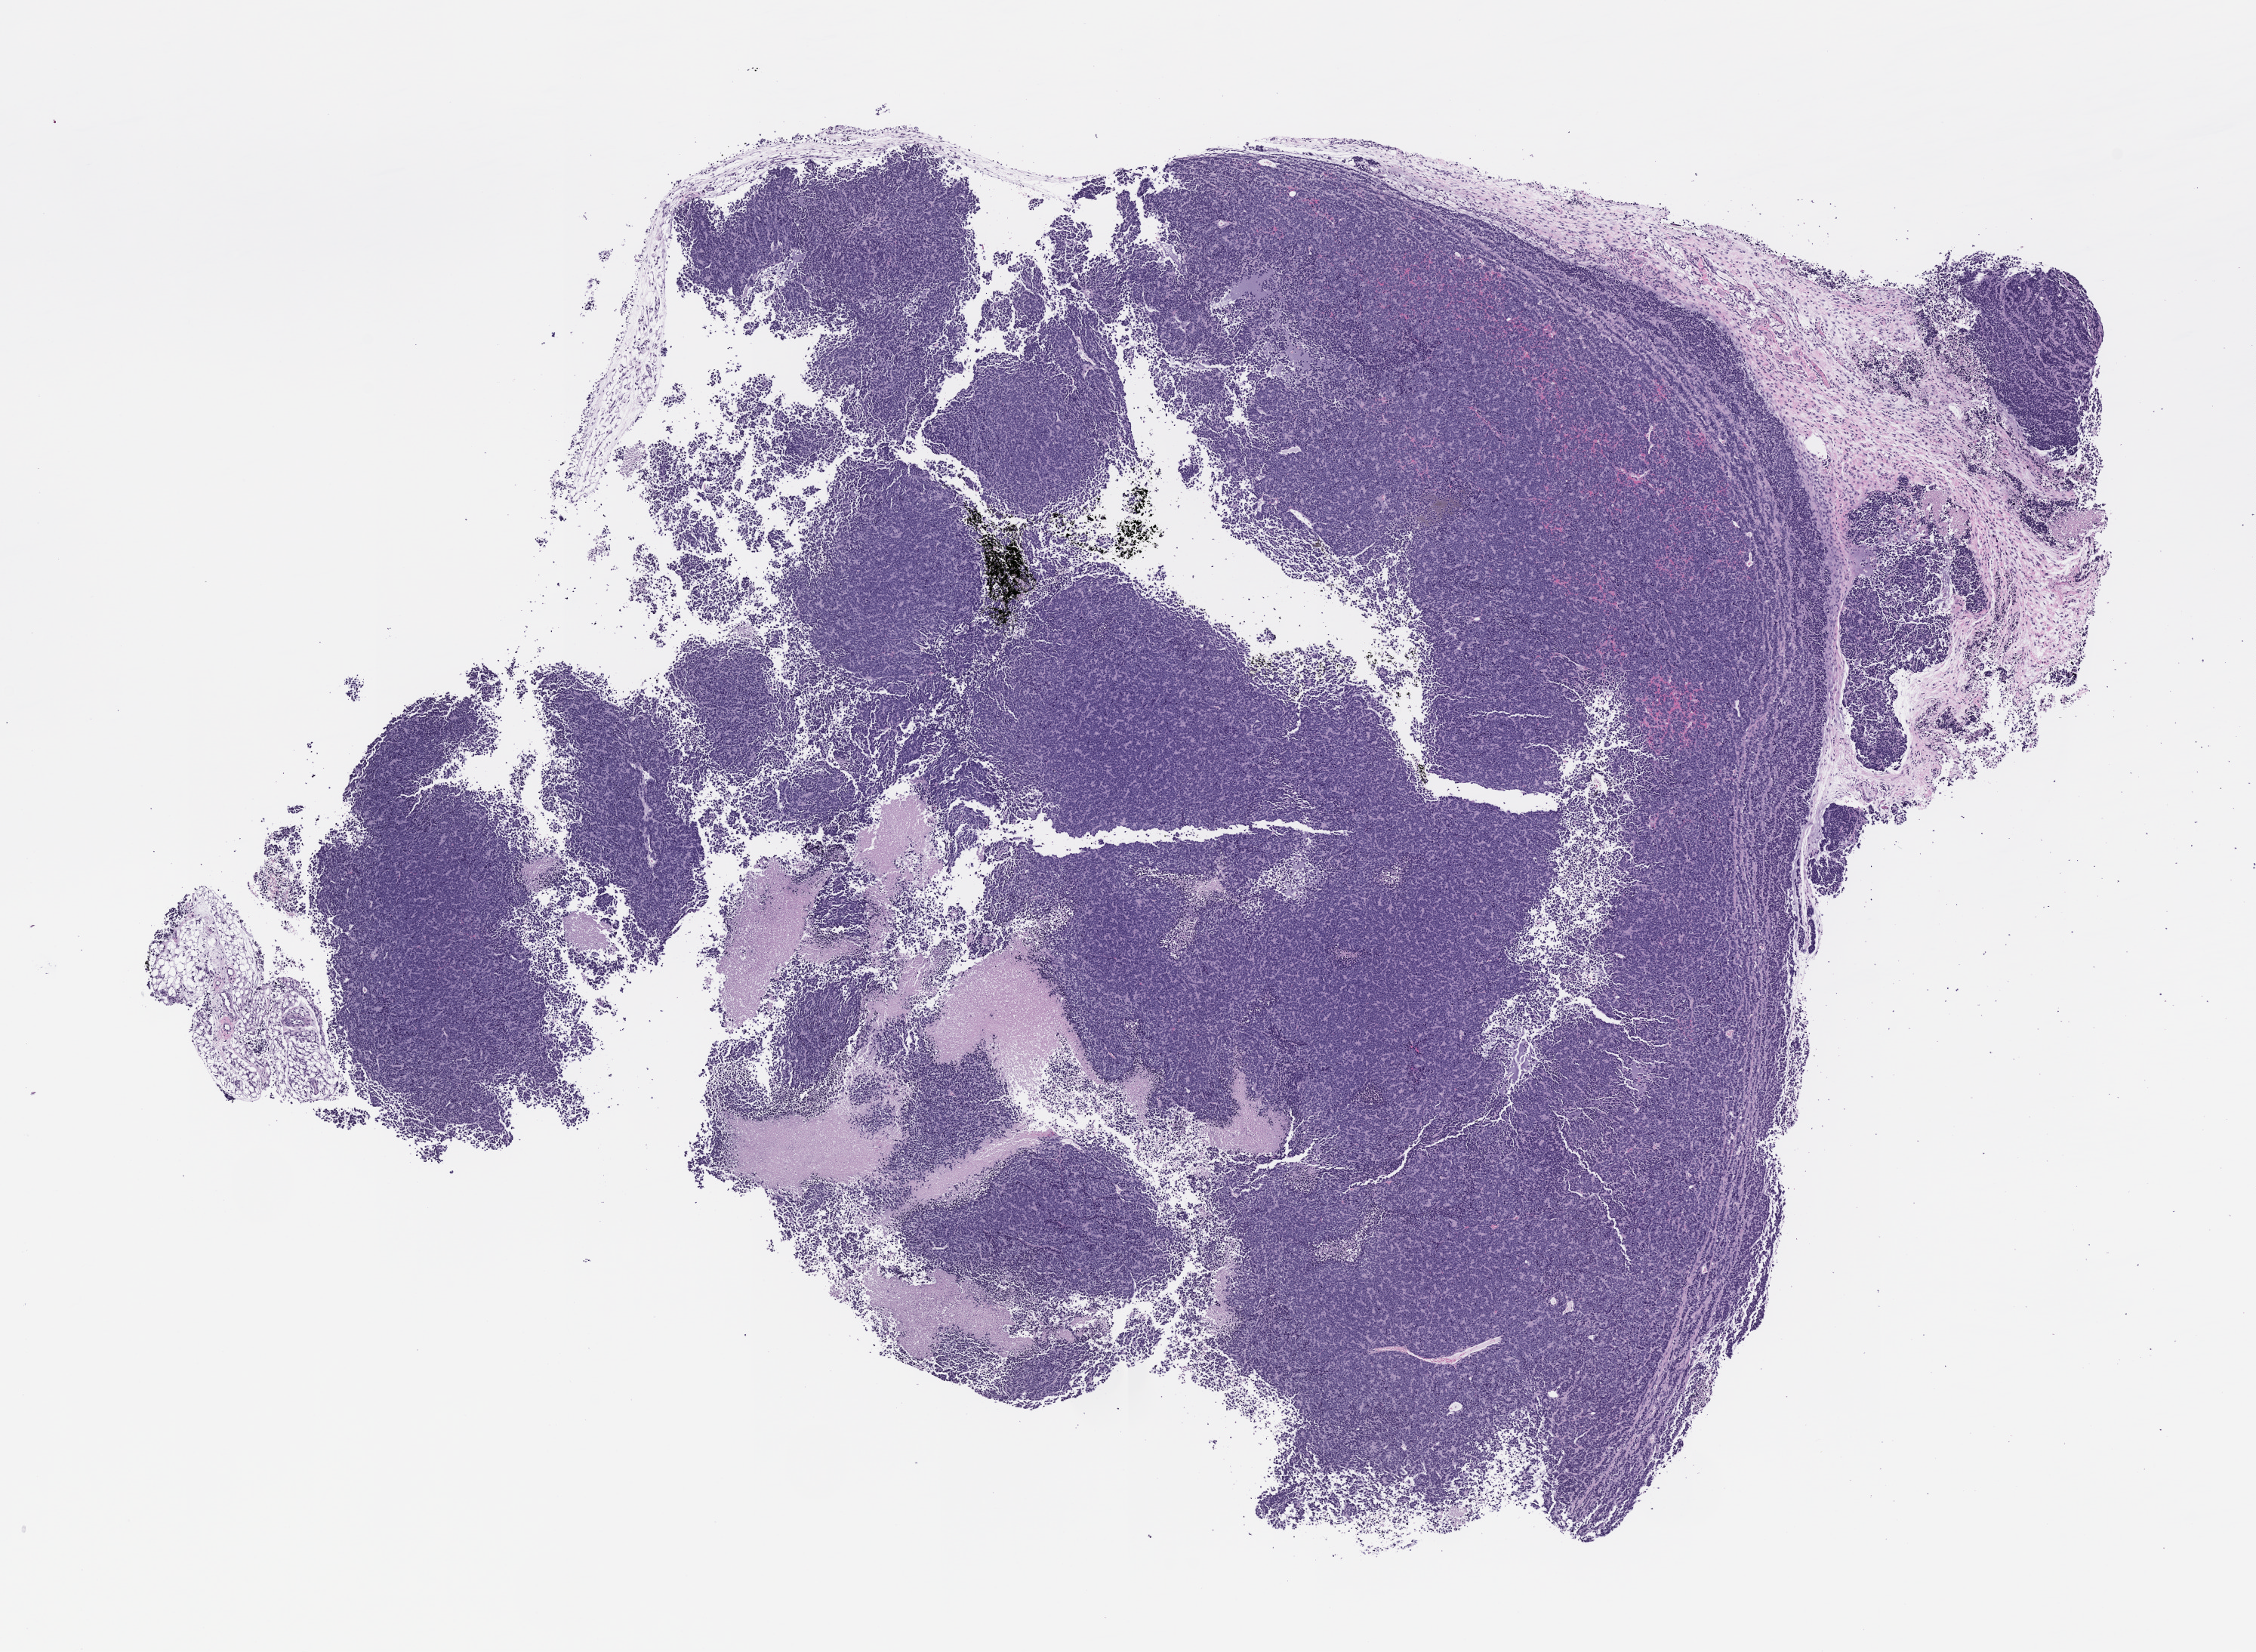
Whole-slide image, haematoxylin and eosin: patient-derived xenograft (human tumor grown in a mouse), passage 2, shown as a low-resolution overview of the whole scanned area (about 12.0 x 8.8 mm); FFPE section; originating tumor site category: musculoskeletal.
Originating patient diagnosis: Ewing Sarcoma|Primitive Neuroectodermal Tumor.